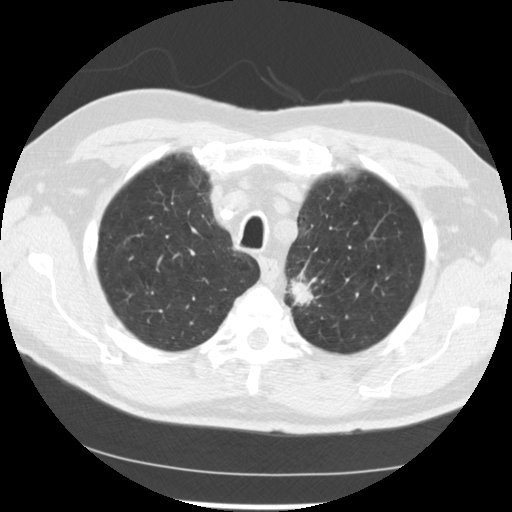
Axial slice from a low-dose chest CT screening exam; baseline annual screen; lung window (W 1500 / L -600 HU); 2.5 mm slice thickness; 120 kVp; 512 × 512 image matrix, field of view 341 × 341 mm. Male, age 71 years at enrolment. Current smoker at enrolment.
• Lesion marked by an expert reader, bounding box <274,263,335,317> (left, top, right, bottom; pixels).
• The screening reader recorded 2 non-calcified nodules or masses ≥4 mm on this exam (left upper lobe, left upper lobe); which of them this box marks is not recorded.
• Later outcome: lung cancer diagnosed 37 days after this screen — adenocarcinoma, NOS, left upper lobe, poorly differentiated (G3), stage IIIB (AJCC 6th edition), 25 mm at pathology.